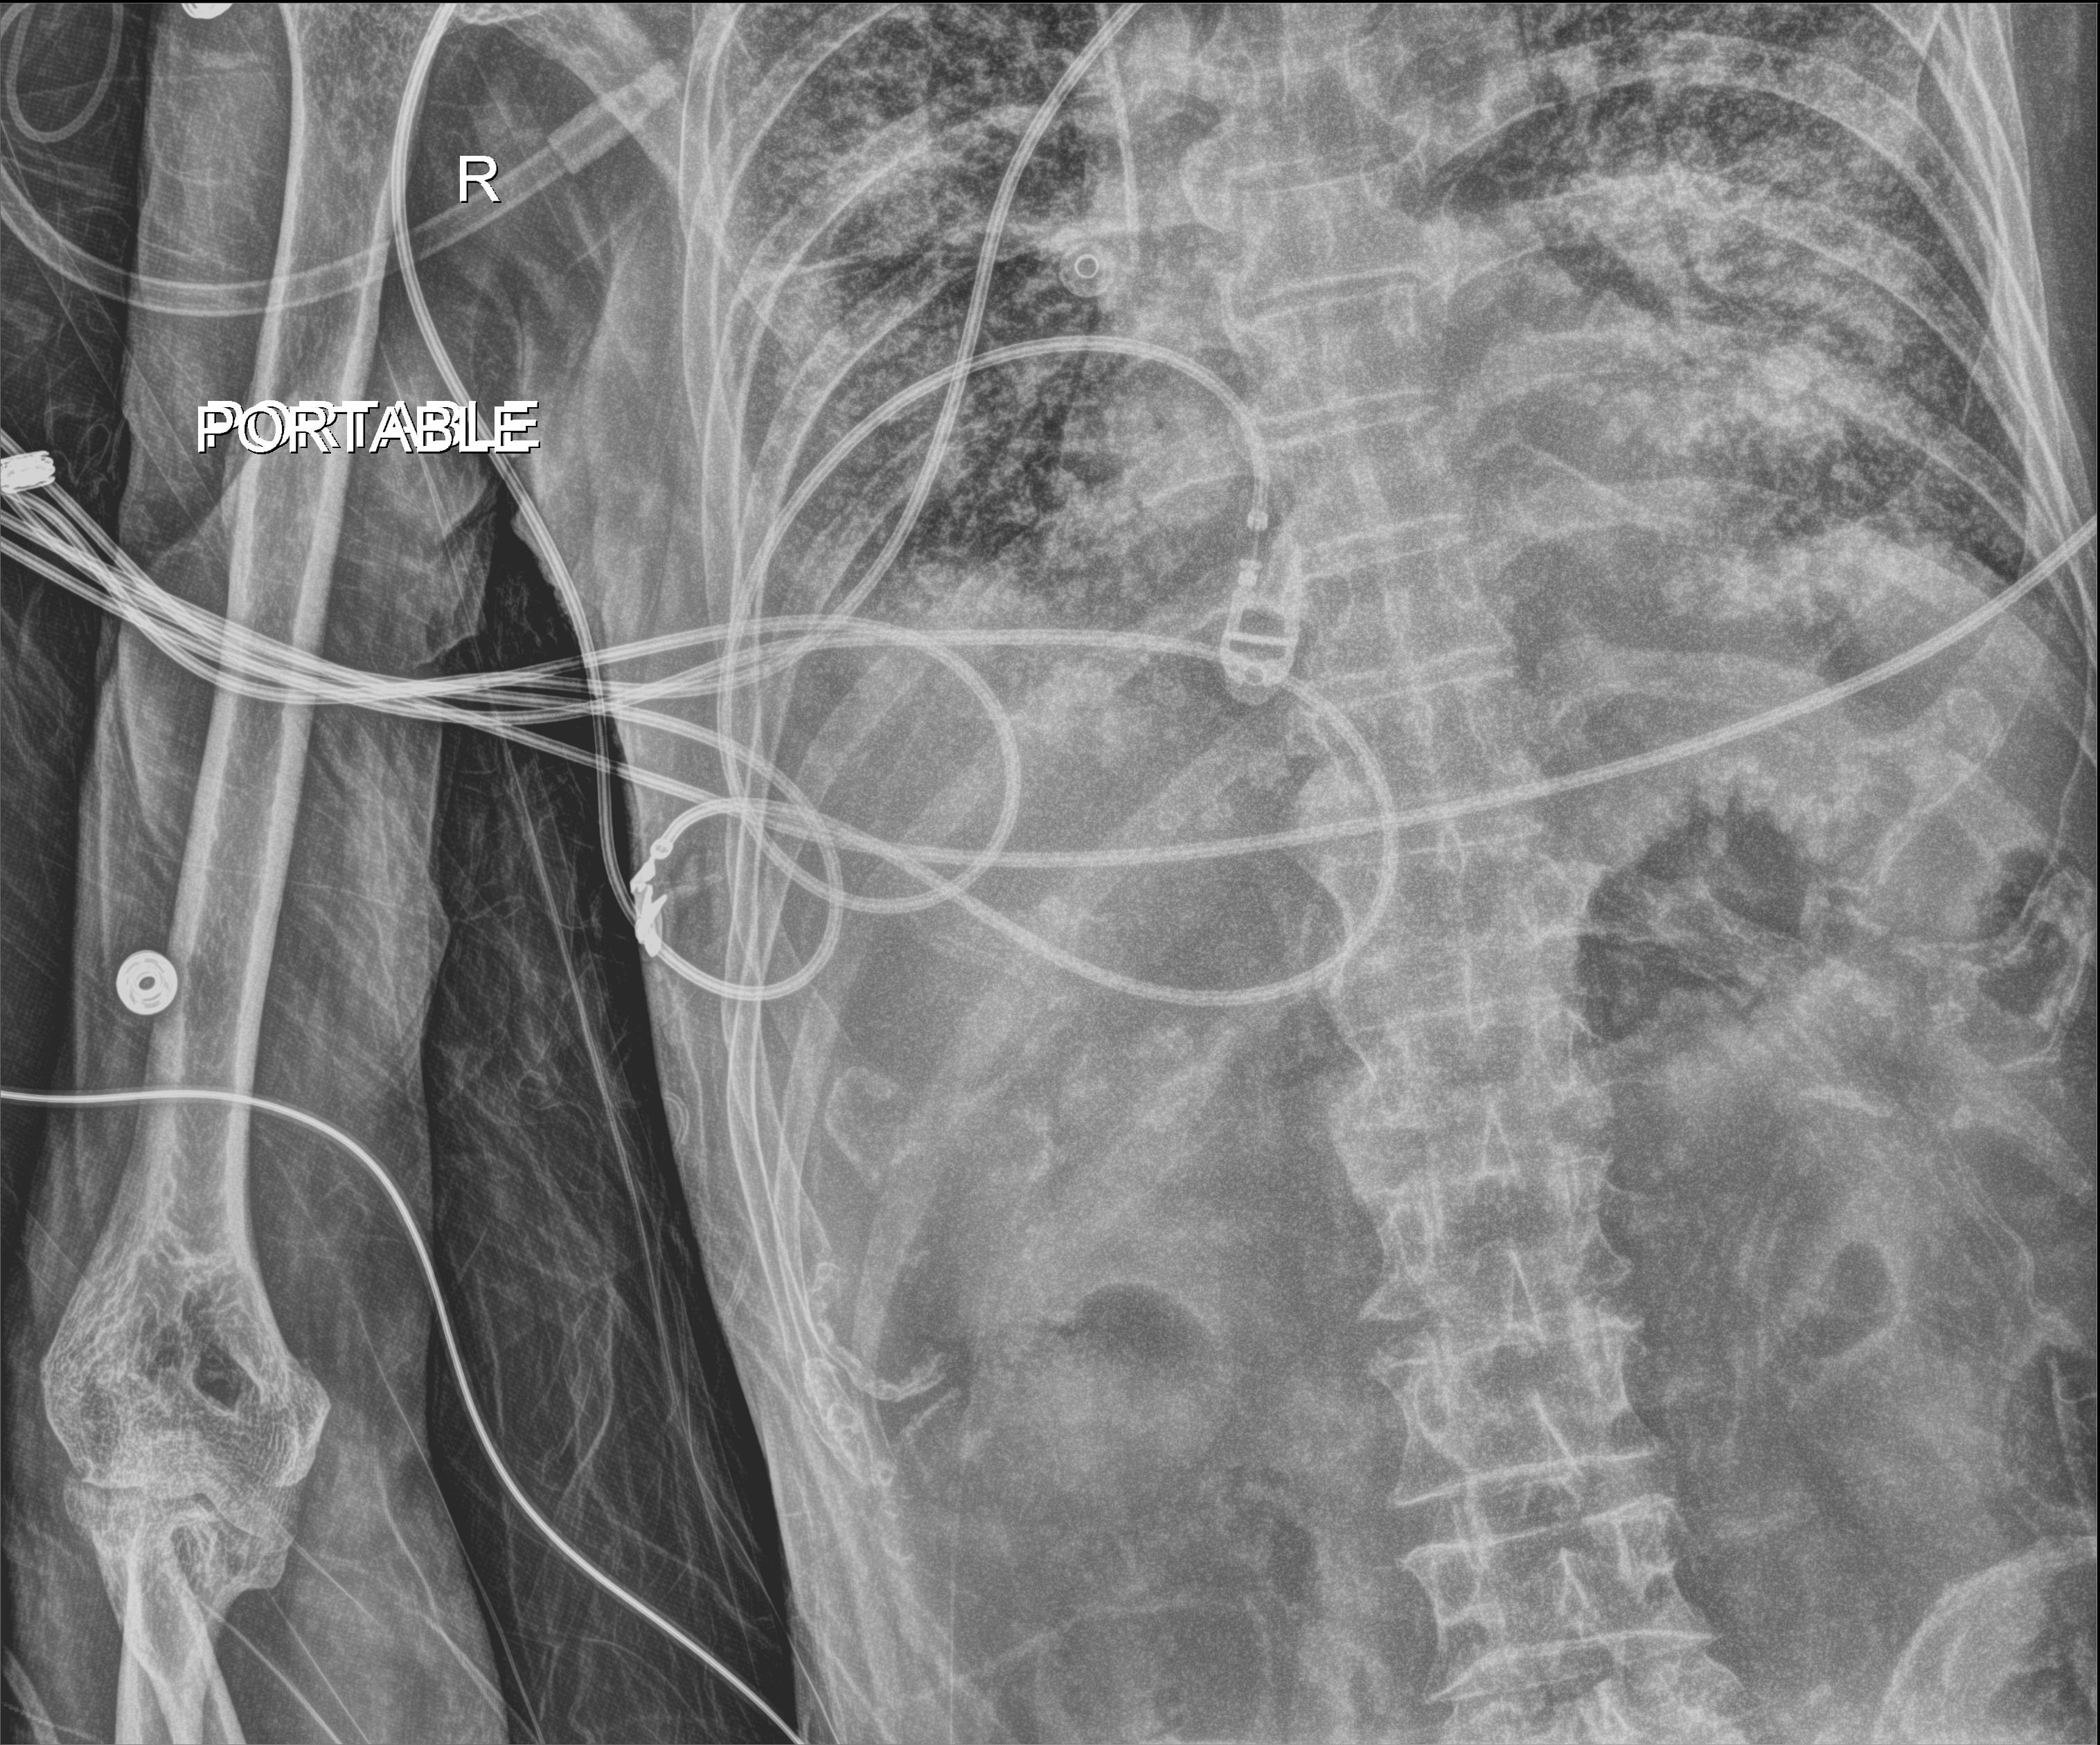
Chest X-ray (portable), anteroposterior (AP) projection. Male patient hospitalised with COVID-19, age 60–74 years.
From the hospital-stay record, not from the radiograph (when in the stay this image was taken is not recorded): COPD (admission record): no.